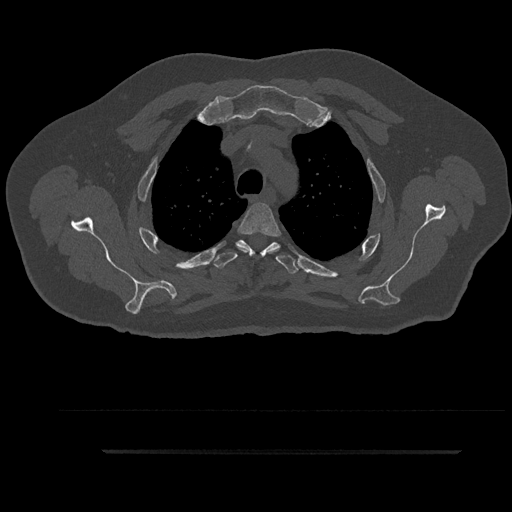
CT including the spine, one axial slice; position 699 of 797 along the scan axis; reconstruction kernel Br40s/3; bone window (W 1800 / L 400 HU); 512 × 512 image matrix, field of view 432 × 432 mm. Patient: male, 63 years. Case-level facts recorded for this patient, not image findings: primary cancer: renal; vertebrae with lytic lesions (as recorded): T8.
Structures marked on this image (semi-automatic segmentation, software-assisted and operator-edited):
- T3 vertebra: box from (x=236, y=202) to (x=281, y=255) px
- T4 vertebra: (x=209, y=239)–(x=299, y=274)